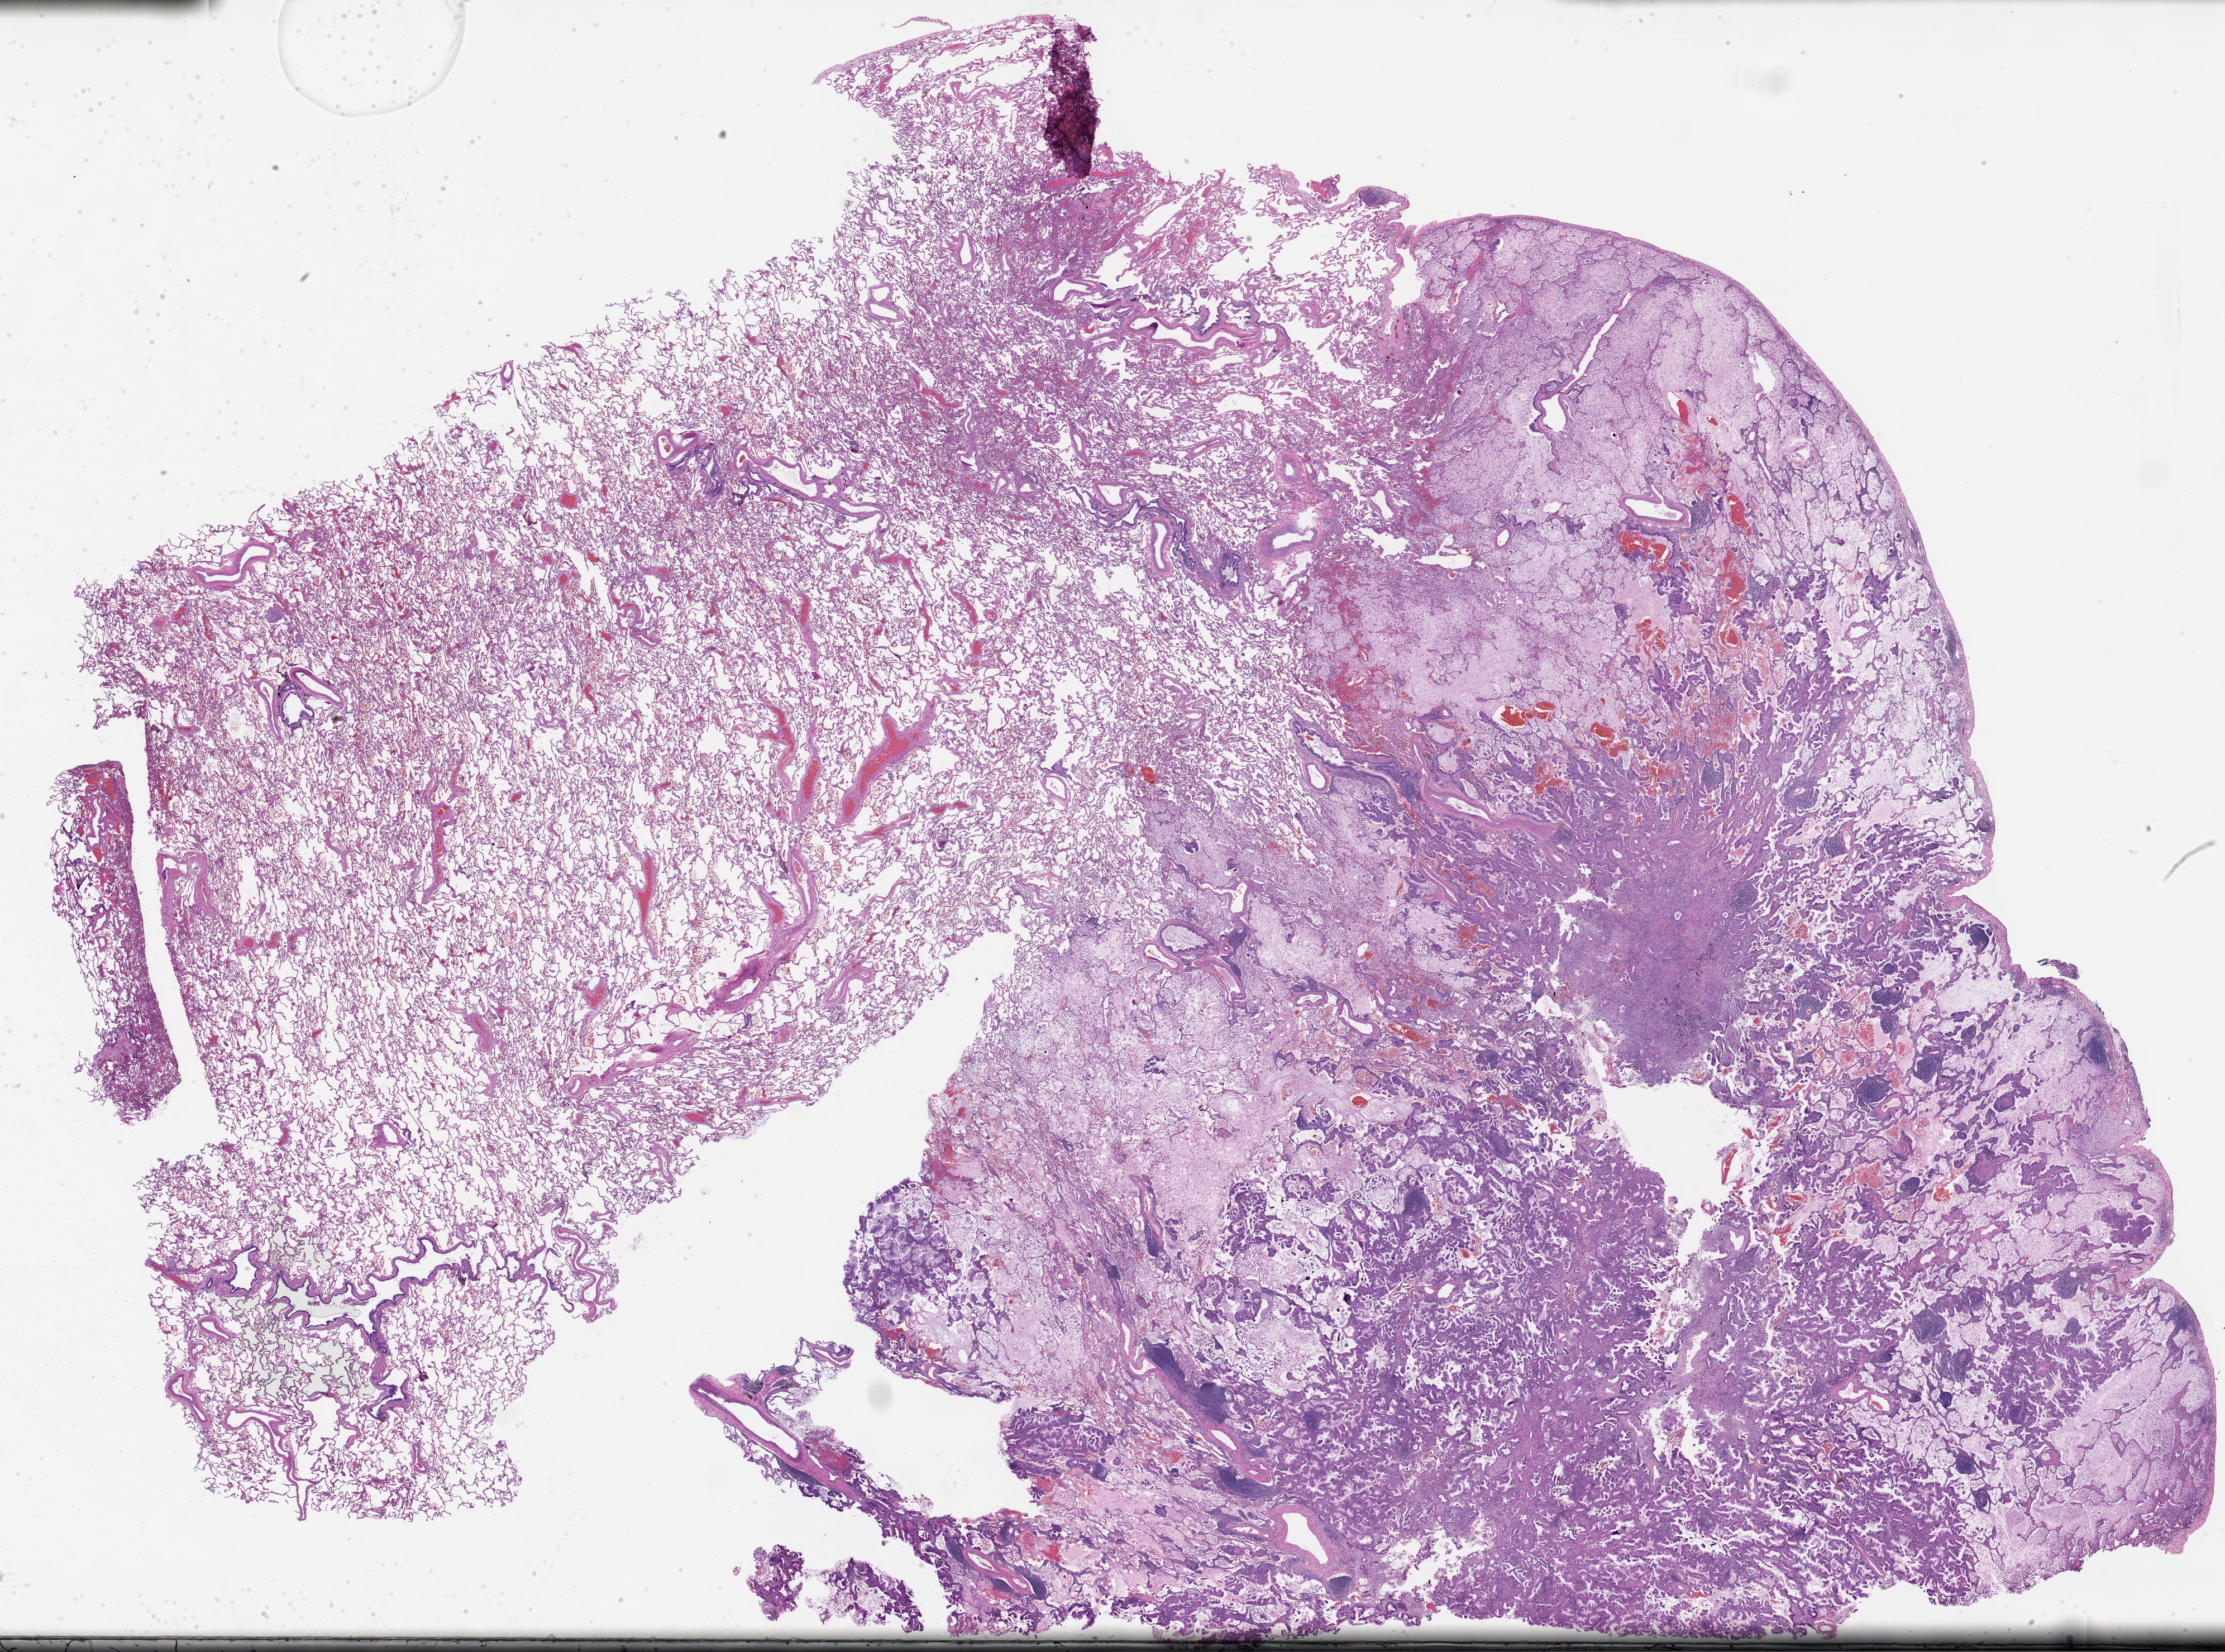
Digitized haematoxylin and eosin-stained section — whole scanned area (about 32.0 x 23.8 mm) shown as a low-resolution overview; FFPE section; specimen: primary tumor; site: lower lobe of left lung. Patient: male, age at initial diagnosis 72 years. Tumor grade: G2 (moderately differentiated). Slide review estimates, as recorded: tumor cells 25%, tumor nuclei 25%, stromal cells 0%, necrosis 0%, normal cells 75%. Infiltration values recorded for this section: lymphocyte infiltration 0%, monocyte infiltration 0%, neutrophil infiltration 0%.
* diagnosis: Adenocarcinoma of lung, mucinous
* AJCC pathologic stage: Stage IB